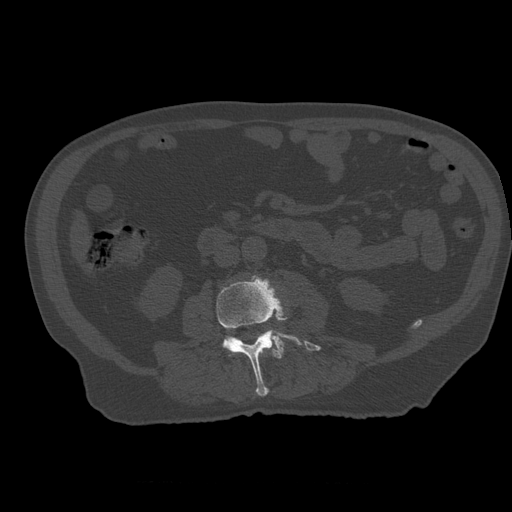
CT including the spine, one axial slice. Slice 187 of 399 in the series (ordered by position). 120 kVp. Bone window (W 1800 / L 400 HU). 512 × 512 image matrix. Patient age 73 years. From the clinical record (not read from this slice): primary cancer: prostate.
Outlined on this slice (semi-automatically segmented with operator editing):
- L2 vertebra: box from (x=230, y=348) to (x=266, y=358) px
- L3 vertebra: (x=217, y=276)–(x=322, y=397)
- L4 vertebra: (x=226, y=333)–(x=285, y=353)